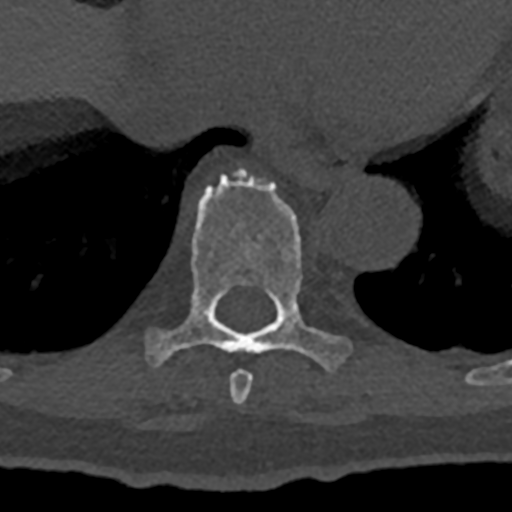
CT including the spine, one axial slice; position 660 of 797 along the scan axis; bone window (W 1800 / L 400 HU); 0.5 mm slice thickness; 512 × 512 image matrix, field of view 160 × 160 mm. Patient: male, 74 years. From the clinical record (not read from this slice): primary cancer: renal; vertebrae with lytic lesions (as recorded): T10, L1, L2, L3, L4, L5.
Annotated regions visible in this slice (semi-automatic segmentation, software-assisted and operator-edited):
- T8 vertebra: box from (x=230, y=370) to (x=253, y=404) px
- T9 vertebra: (x=145, y=169)–(x=352, y=372)